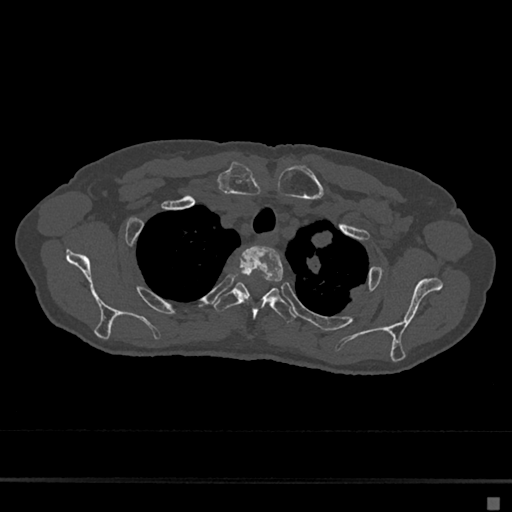
CT including the spine, one axial slice. Slice 557 of 797 in the series (ordered by position). Reconstruction kernel Br40s/3. 120 kVp. Bone window (W 1800 / L 400 HU). 0.5 mm slice thickness. 512 × 512 image matrix, field of view 360 × 360 mm. Patient: female, 68 years. Case-level facts recorded for this patient, not image findings: primary cancer: renal.
Structures marked on this image (semi-automatically segmented with operator editing):
- T2 vertebra: box from (x=236, y=246) to (x=284, y=295) px
- T3 vertebra: (x=213, y=282)–(x=296, y=323)